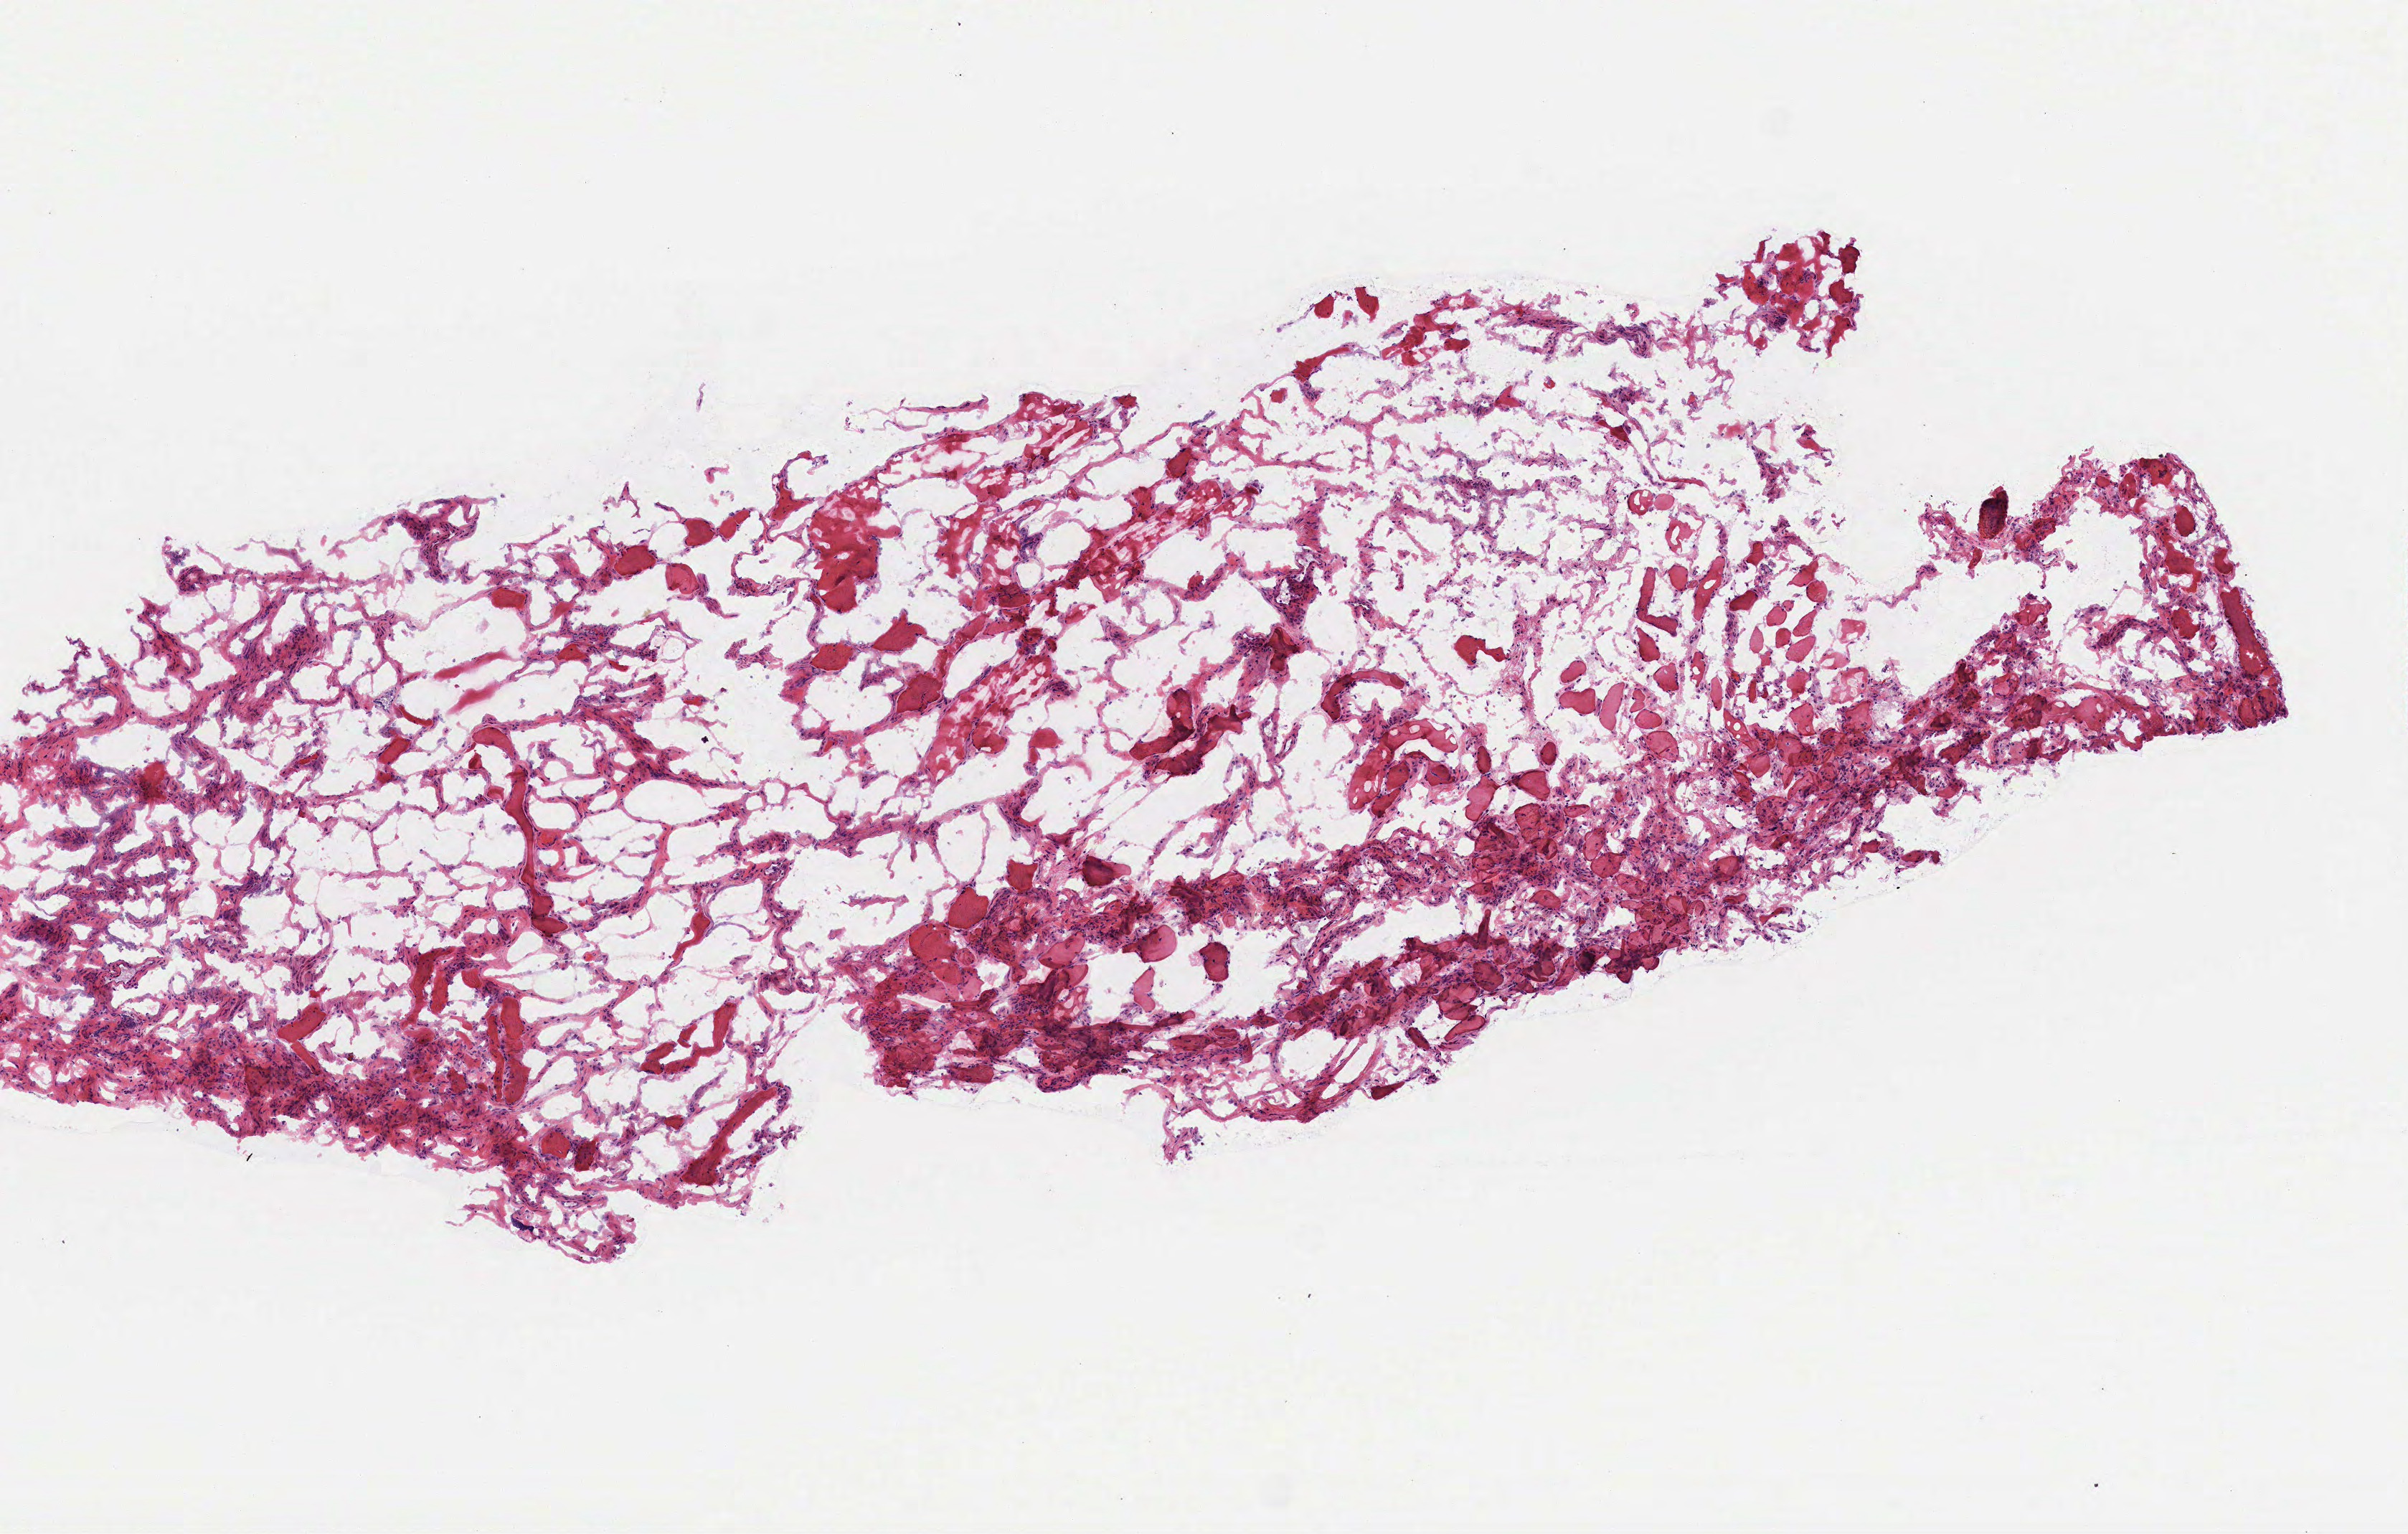
Digitized H&E tissue section (whole slide), a low-resolution overview of the entire scanned area, about 6.8 x 4.3 mm (acquisition: 40x scan), frozen section from the top of the tissue portion, sample: solid tissue normal (non-tumour tissue), head and neck. Male patient; age at initial diagnosis 62 years.
This section: solid tissue normal (non-tumour) sample from the same patient. Patient diagnosis: Squamous cell carcinoma, NOS (larynx, NOS).